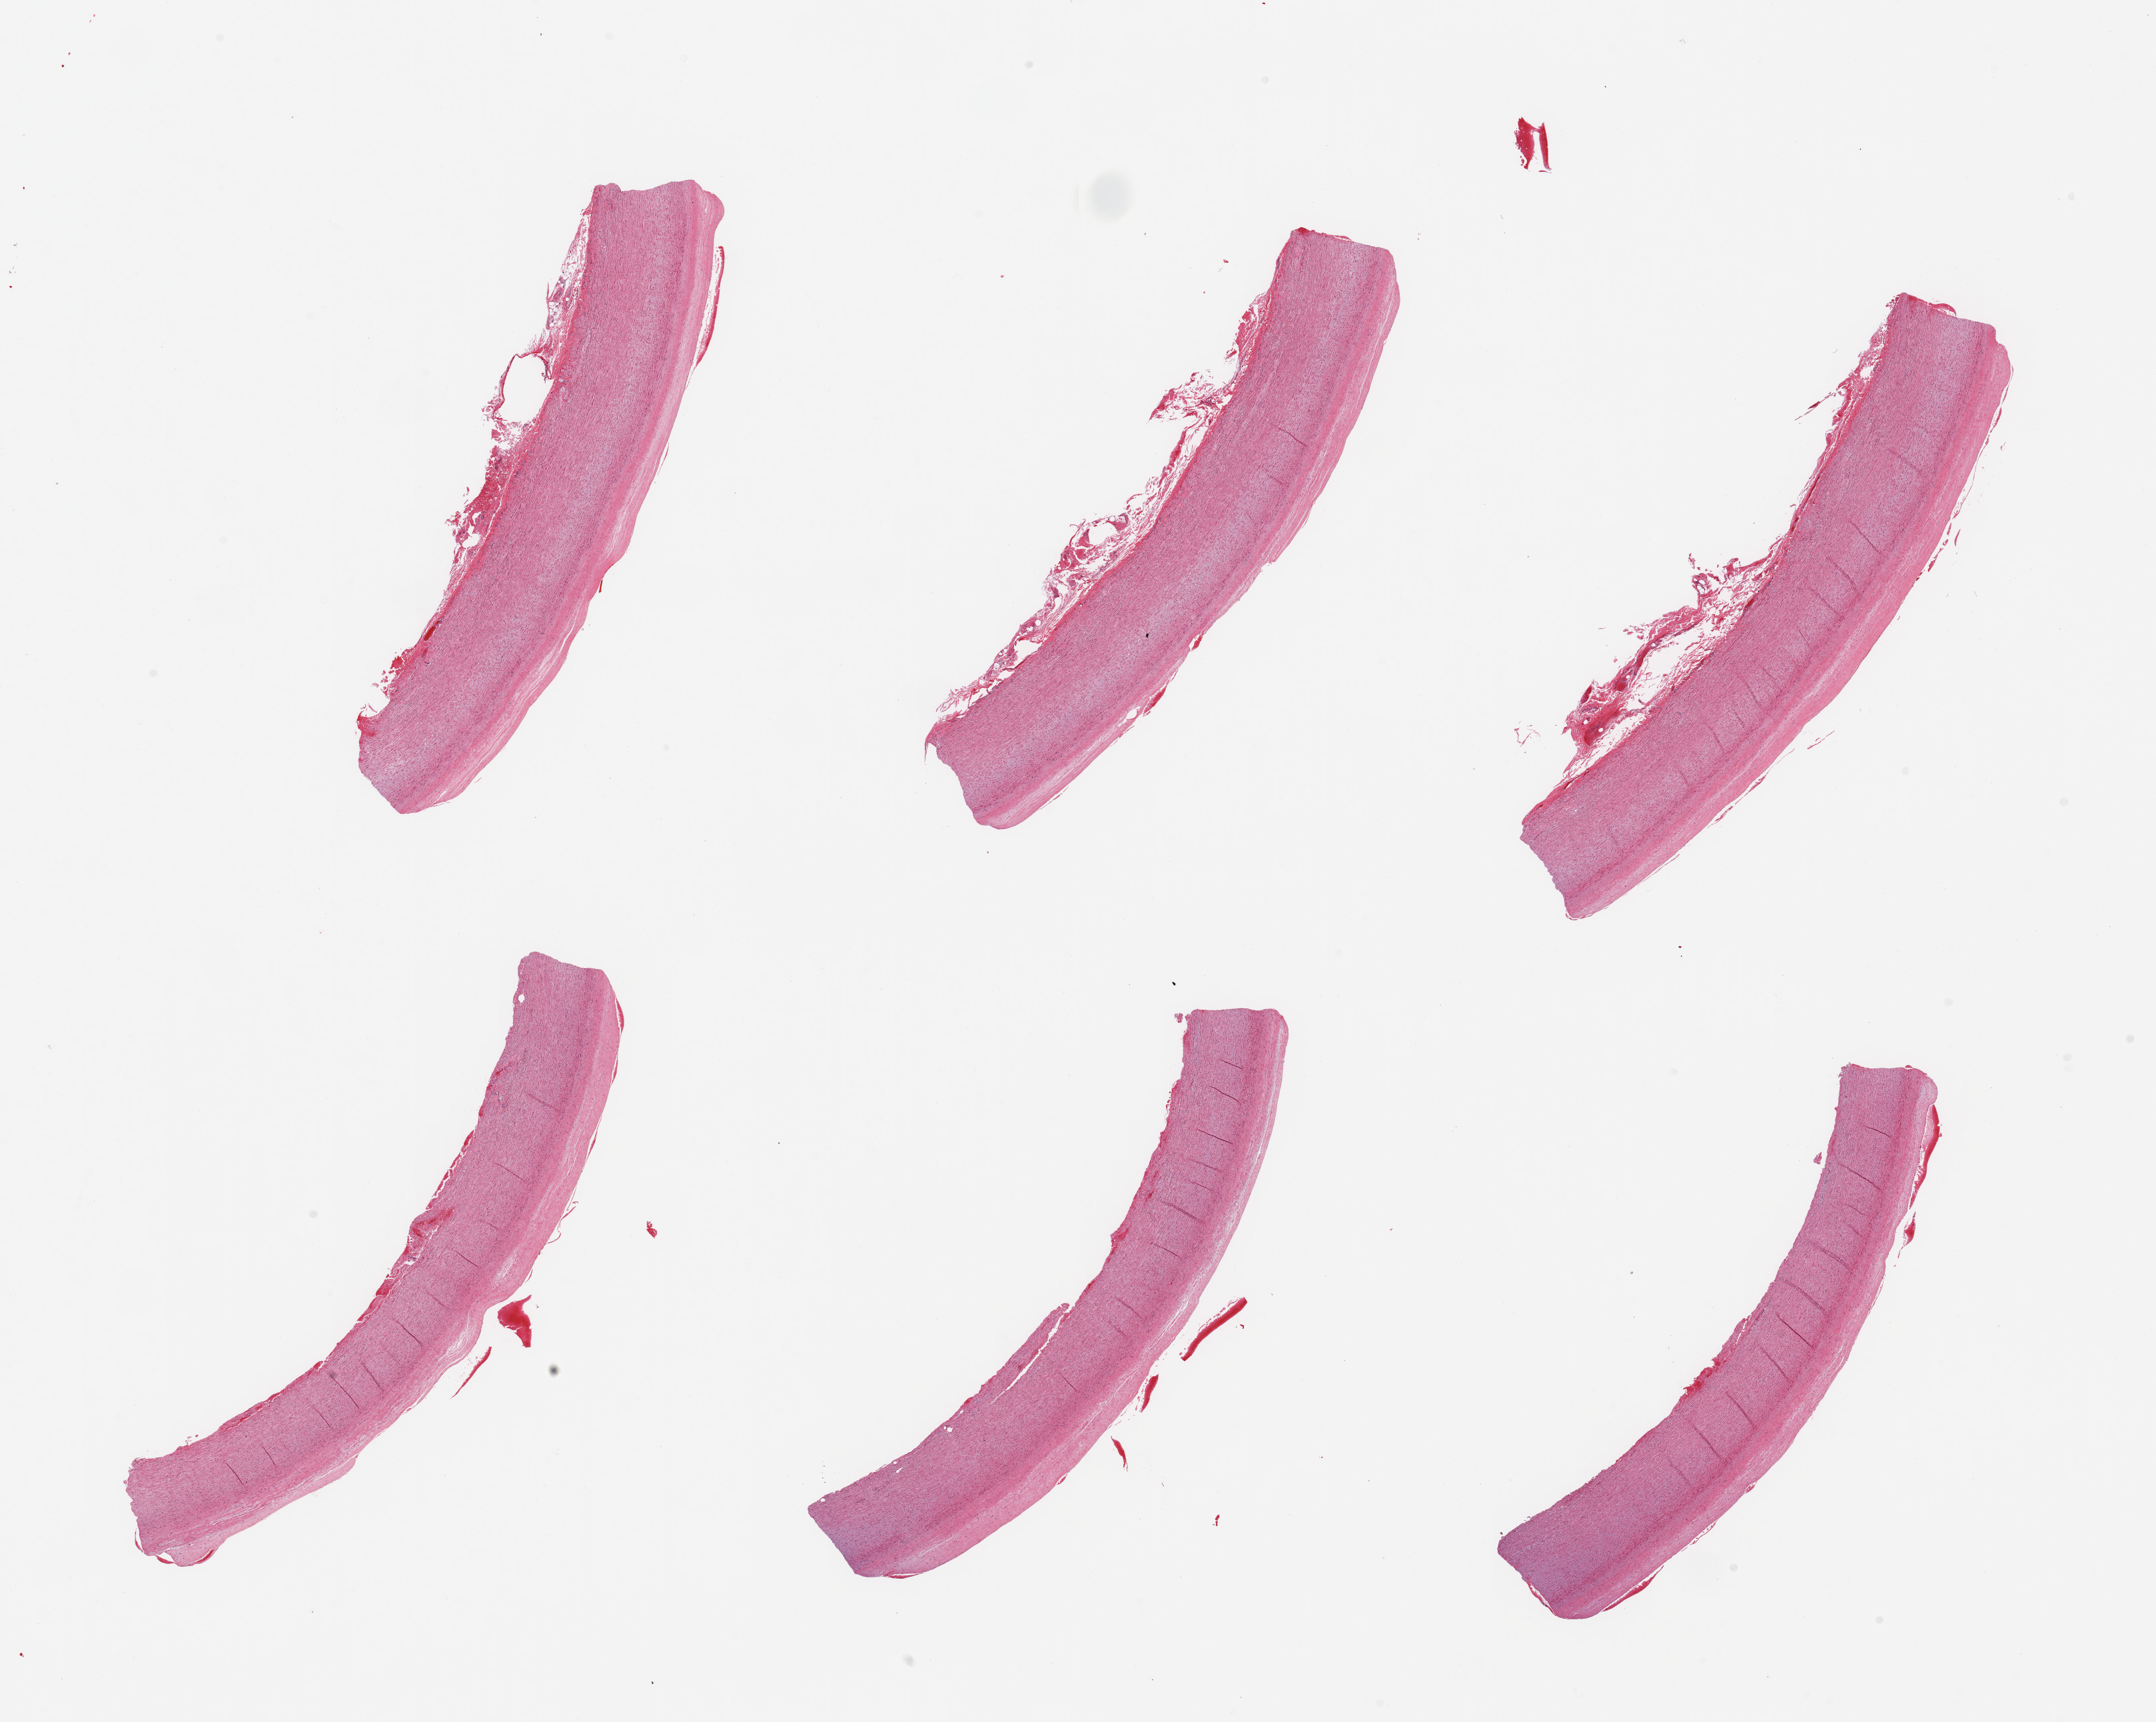
Whole-slide image, hematoxylin and eosin (H&E) stain, brightfield — shown as a low-resolution overview of the whole scanned area (about 25.6 x 20.4 mm, slide scanned at 20x), PAXgene-fixed paraffin-embedded (PFPE) section, section of aorta (target tissue), tissue donor sample. Donor sex: female.
Pathologist's review note for this sample: 6 pieces; slight flat plaques; well trimmed.